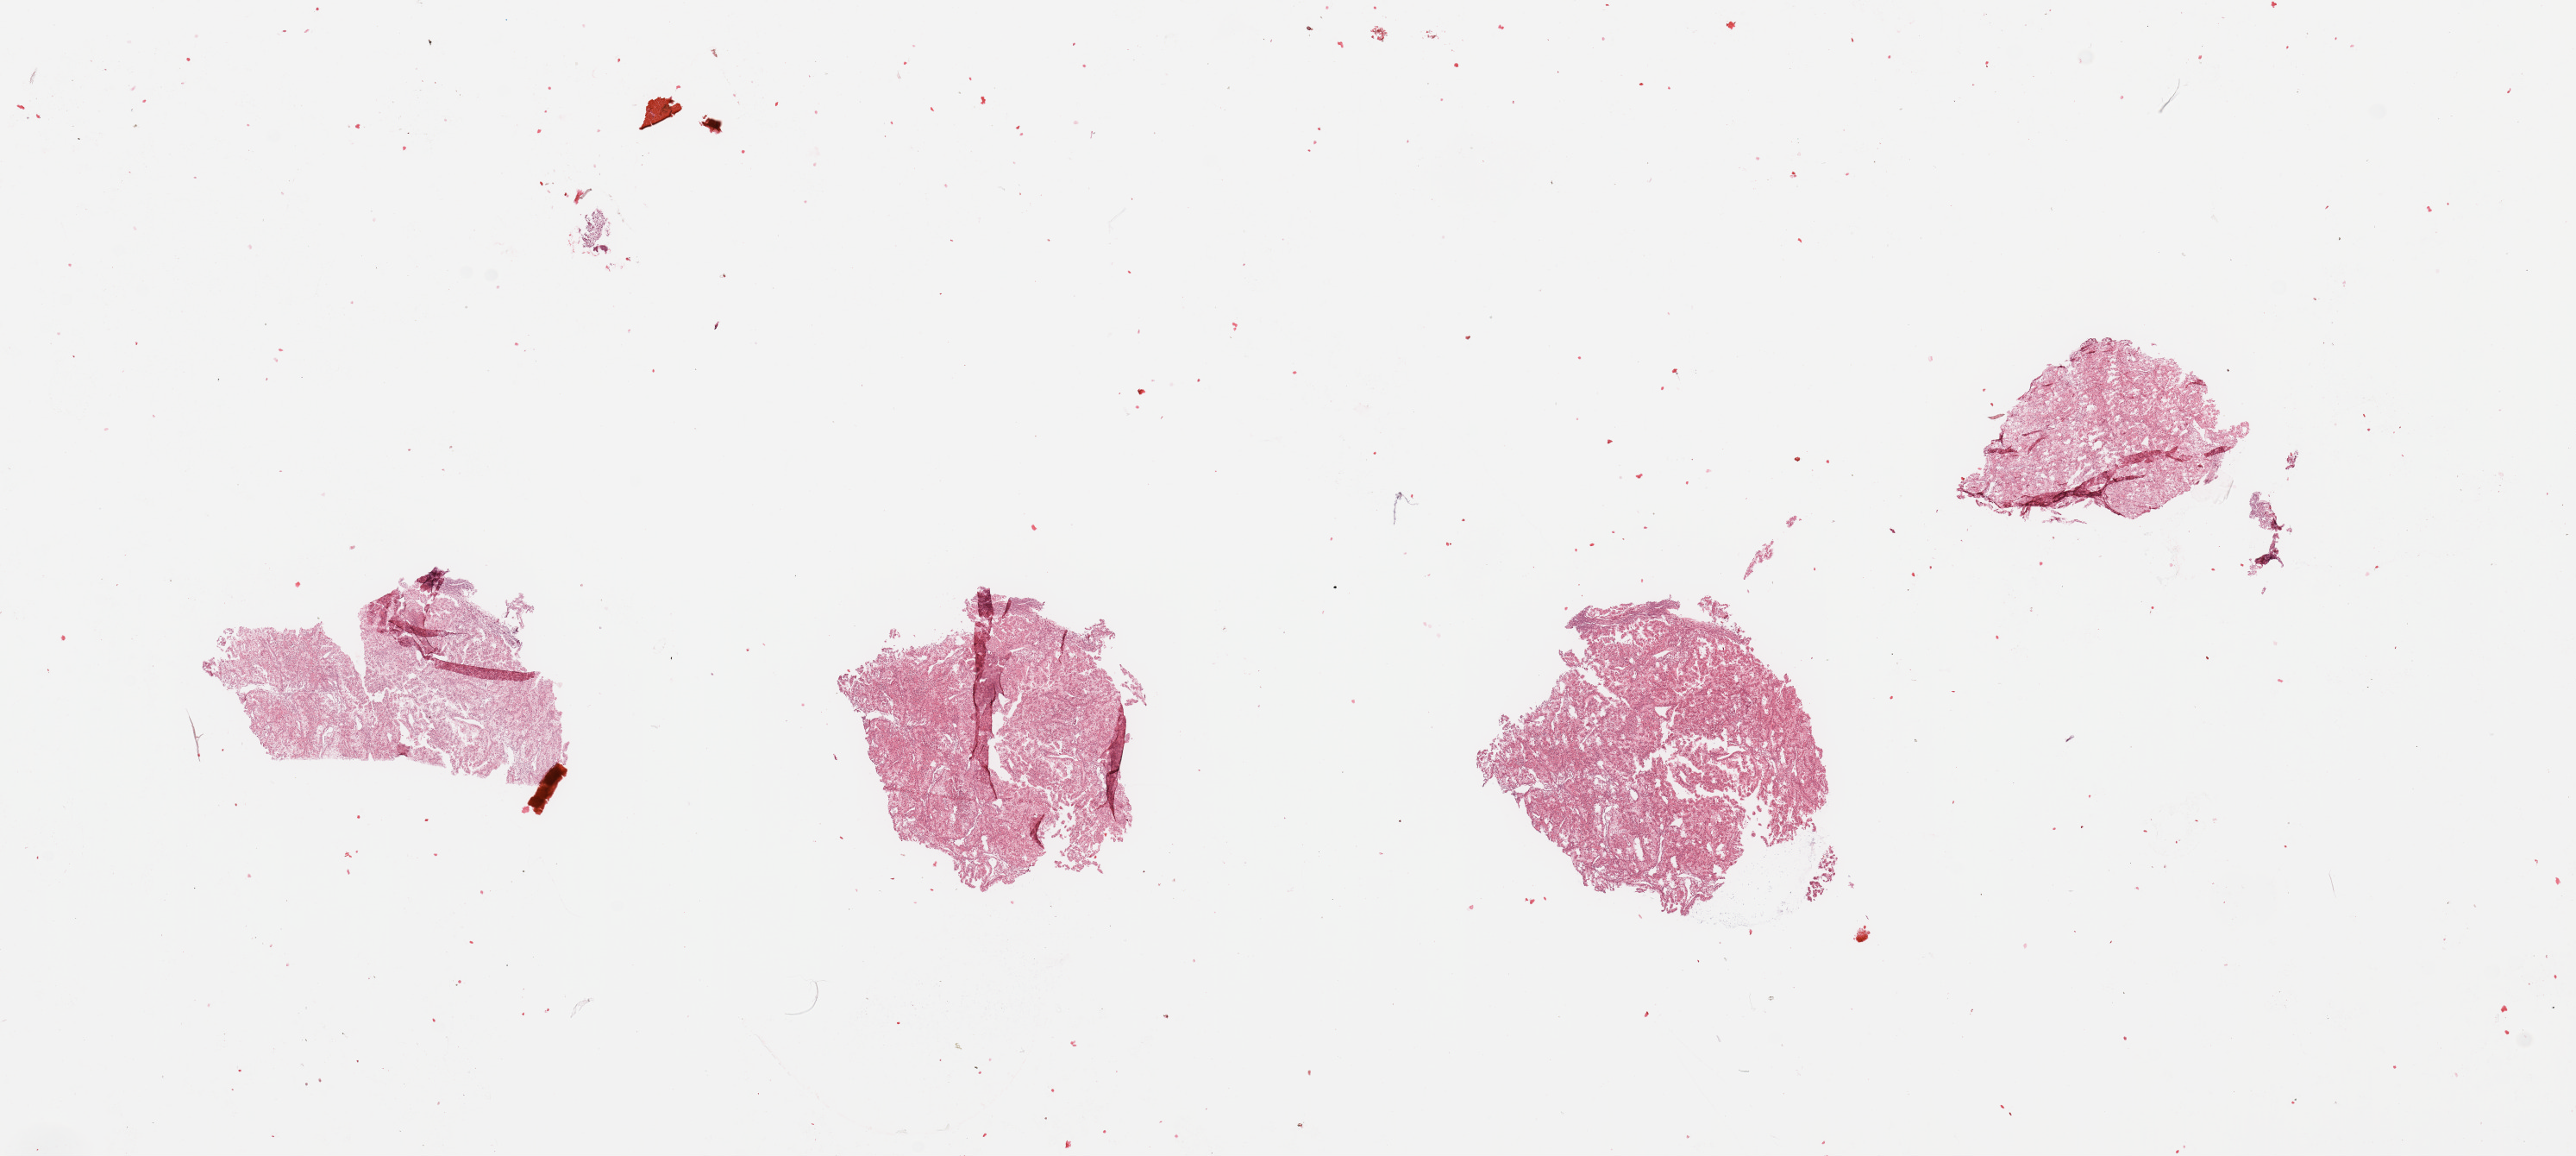
Digitized Hematoxylin and eosin (H&E) stained tissue section (whole slide), whole scanned area (about 23.6 x 10.6 mm, acquisition: 20x scan) shown as a low-resolution overview; kidney, tumour tissue. Patient: male, age 64 years.
Histologic diagnosis: Renal cell carcinoma, NOS.